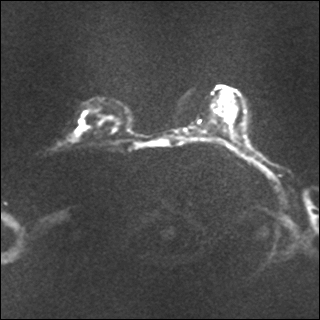
Breast MRI, one axial slice. Position 19 of 35 along the scan axis. Diffusion-weighted series; image 2 of 4 stored at this slice position (different b-values; order by instance number). 1.5 T. 4 mm slice thickness. 320 × 320 image matrix, field of view 317 × 317 mm. Female patient.
Structures marked on this image (expert manual segmentation):
- tumour on diffusion-weighted imaging: bounding box <76,118,84,139> (left, top, right, bottom; pixels)